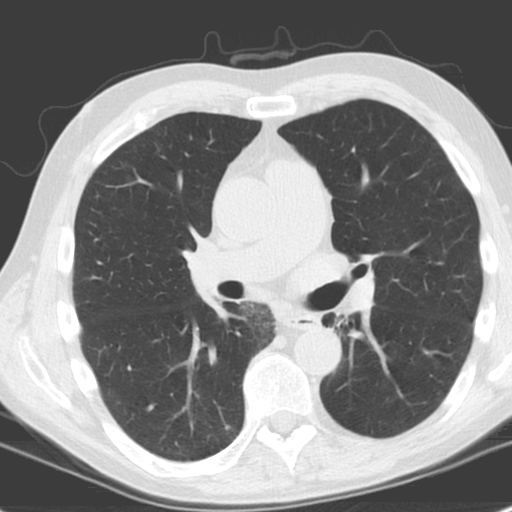
Low-dose screening chest CT, axial slice; baseline screening round; lung window (W 1500 / L -600 HU); 3.2 mm slice thickness; slice 82 of 185 in the series. Male, age 61 years at enrolment. Former smoker at enrolment.
• Expert reader's lesion annotation, bounding box <313,308,362,344> (left, top, right, bottom; pixels).
• No non-calcified nodule or mass ≥4 mm was recorded by the screening reader at this exam.
• Official screen result: negative screen, minor abnormalities not suspicious for lung cancer.
• Lung cancer was diagnosed 1146 days after this screen (after the third annual screen): squamous cell carcinoma, NOS, left upper lobe, left lower lobe, well differentiated (G1), stage IIB (AJCC 6th edition), 100 mm at pathology.